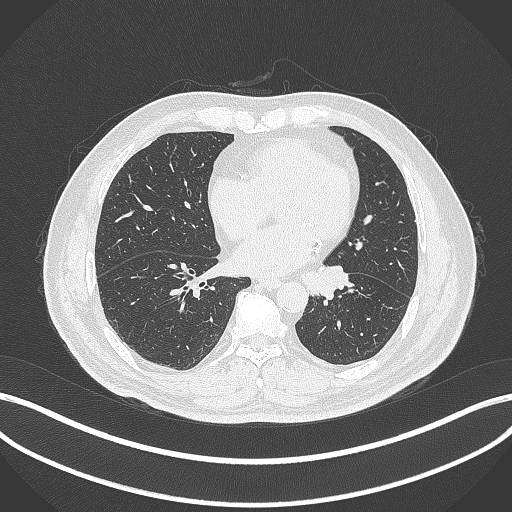
Chest CT, one axial slice. Position 110 of 312 along the scan axis. Lung window (W 1500 / L -600 HU). 1 mm slice thickness. 512 × 512 image matrix, field of view 400 × 400 mm. Male patient, age 71 years. From the clinical record (not read from this slice): clinical TNM (as recorded): T1b N0 M0.
Annotated regions visible in this slice (bounding box drawn by a radiologist):
- lung tumour (recorded histology: squamous cell carcinoma): bounding box [x1, y1, x2, y2] px = [300, 265, 354, 300]